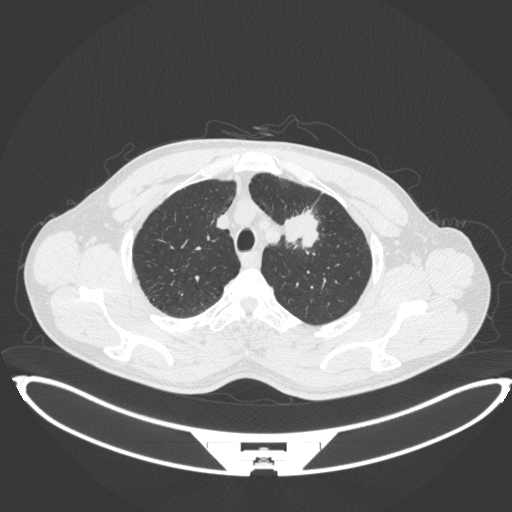
Chest CT, one axial slice. Slice 360 of 407 in the series (ordered by position). Reconstruction kernel B31f. 120 kVp. Lung window (W 1500 / L -600 HU). 512 × 512 image matrix, field of view 457 × 457 mm. Patient: male, 60 years. From the clinical record (not read from this slice): clinical TNM (as recorded): T2a N0 M0; histopathological grade: G1-G2.
Outlined on this slice (bounding box drawn by a radiologist):
- lung tumour (recorded histology: squamous cell carcinoma): bounding box (x1, y1, x2, y2) in pixels: (284, 205, 321, 253)